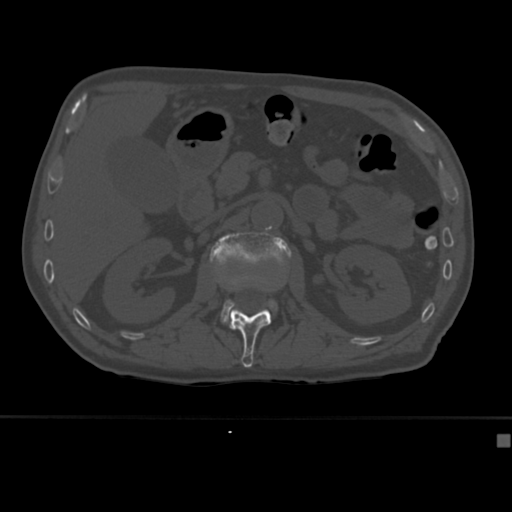
CT including the spine, one axial slice. Slice 162 of 430 in the series (ordered by position). Bone window (W 1800 / L 400 HU). 512 × 512 image matrix, field of view 337 × 337 mm. Male patient, age 64 years. From the clinical record (not read from this slice): primary cancer: uterus; vertebrae with lytic lesions (as recorded): T1, T4, T5, T7, L5.
Structures marked on this image (semi-automatically segmented with operator editing):
- L1 vertebra: box from (x=227, y=279) to (x=282, y=368) px
- L2 vertebra: (x=210, y=232)–(x=292, y=323)